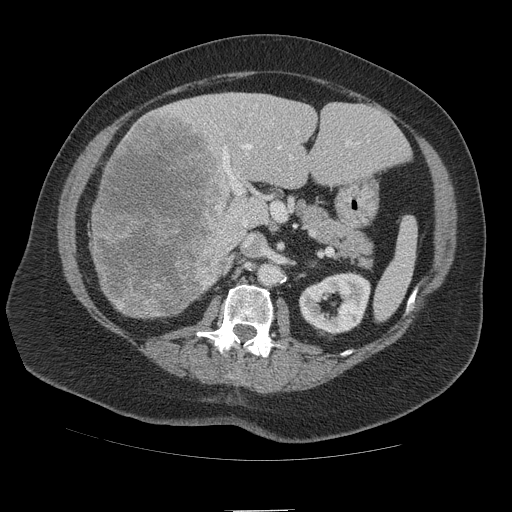
Contrast-enhanced abdominal CT (liver protocol), one axial slice. Slice 52 of 109 in the series (ordered by position). Reconstruction kernel STANDARD. Soft-tissue window (W 400 / L 40 HU). 2.5 mm slice thickness. 512 × 512 image matrix. Case-level facts recorded for this patient, not image findings: diagnosis: hepatocellular carcinoma (patient treated with transarterial chemoembolisation; whether this scan precedes or follows treatment is not stated here); TNM stage (as recorded): Stage-IVB; Child-Pugh class: A.
Structures marked on this image (semi-automatic segmentation, software-assisted and operator-edited):
- liver parenchyma outside the tumour (the mass and vessels are separate outlines, so this box may not span the whole liver): bounding box (x1, y1, x2, y2) in pixels: (92, 92, 410, 318)
- mass: (90, 108, 246, 319)
- liver vessels: (223, 141, 358, 226)